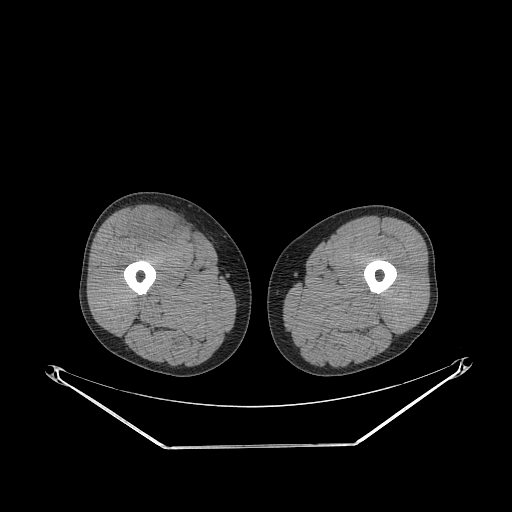
CT of an extremity soft-tissue mass (from a PET/CT study), one axial slice. Slice 261 of 311 in the series (ordered by position). 140 kVp. Soft-tissue window (W 400 / L 40 HU). 512 × 512 image matrix, field of view 500 × 500 mm. Male patient. Case-level facts recorded for this patient, not image findings: histological type: pleiomorphic leiomyosarcoma; grade: intermediate; site of the primary tumour: right thigh.
Outlined on this slice (expert contour drawn on MRI and transferred to this co-registered scan by the dataset authors):
- gross tumour volume including surrounding oedema: bounding box <132,210,179,241> (left, top, right, bottom; pixels)